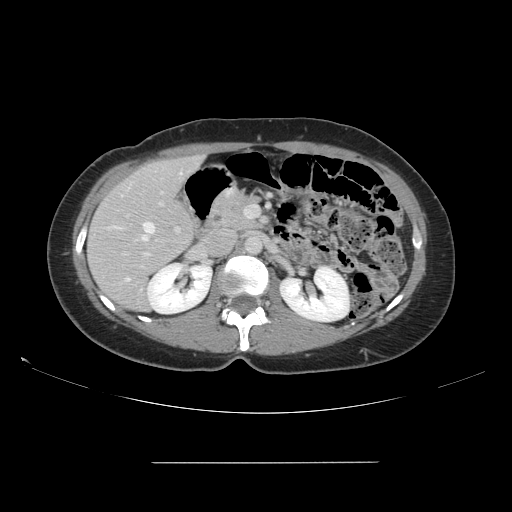
Contrast-enhanced abdominal CT, one axial slice. Slice 80 of 151 in the series (ordered by position). 120 kVp. Intravenous contrast given. Soft-tissue window (W 400 / L 40 HU). 512 × 512 image matrix. Female patient, age 46 years. From the clinical record (not read from this slice): diagnosis: colorectal cancer liver metastases, imaged before liver resection; multiple liver metastases: yes; largest metastasis: 3 cm.
Outlined on this slice (expert manual segmentation):
- hepatic veins: box from (x=115, y=184) to (x=155, y=280) px
- liver: (x=88, y=156)–(x=202, y=311)
- planned liver remnant (the part of the liver to remain after resection): (x=97, y=157)–(x=201, y=312)
- portal vein (with intrahepatic branches): (x=123, y=190)–(x=246, y=260)